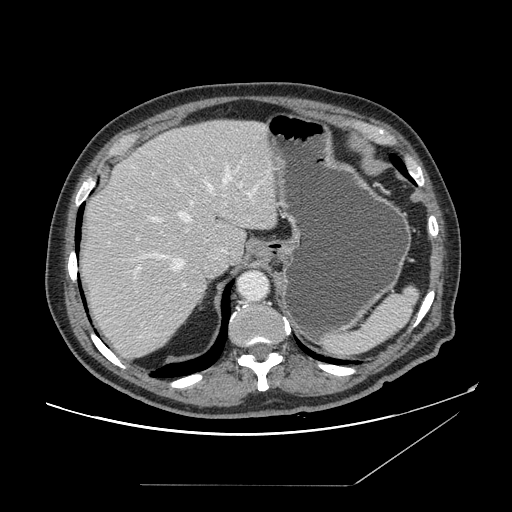
Contrast-enhanced abdominal CT, one axial slice. 120 kVp. Intravenous contrast given. Soft-tissue window (W 400 / L 40 HU). 2.5 mm slice thickness. 512 × 512 image matrix, field of view 416 × 416 mm. Male patient, age 80 years. Case-level facts recorded for this patient, not image findings: diagnosis: colorectal cancer liver metastases, imaged before liver resection; multiple liver metastases: no; largest metastasis: 2.2 cm; chemotherapy before resection: no.
Annotated regions visible in this slice (outlined manually by an expert reader):
- hepatic veins: bounding box [x1, y1, x2, y2] px = [139, 167, 232, 271]
- liver: [79, 120, 278, 358]
- planned liver remnant (the part of the liver to remain after resection): [83, 120, 277, 263]
- portal vein (with intrahepatic branches): [136, 158, 256, 272]